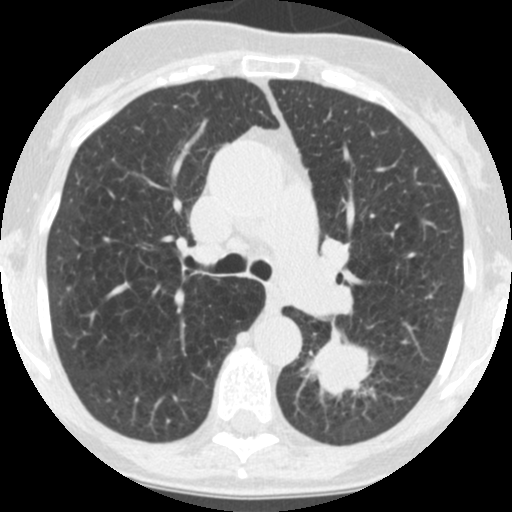
Axial slice from a low-dose chest CT screening exam, third annual screen, lung window (W 1500 / L -600 HU), slice 59 of 171 in the series, 512 × 512 image matrix. Female participant, aged 71 years at enrolment. Current smoker at enrolment.
Expert-annotated lung lesion, bounding box <303,327,383,410> (left, top, right, bottom; pixels). The screening reader recorded 2 non-calcified nodules or masses ≥4 mm on this exam; which of them this box marks is not recorded. Later outcome: lung cancer diagnosed 26 days after this screen — squamous cell carcinoma, NOS, left lower lobe, poorly differentiated (G3), stage IB (AJCC 6th edition), 40 mm at pathology.